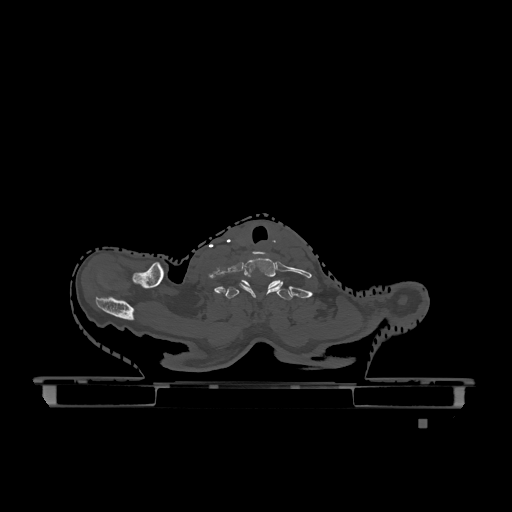
CT including the spine, one axial slice; slice 1017 of 1317 in the series (ordered by position); bone window (W 1800 / L 400 HU); 0.5 mm slice thickness; 512 × 512 image matrix, field of view 500 × 500 mm. Patient: female, 74 years. From the clinical record (not read from this slice): primary cancer: lung; vertebrae with lytic lesions (as recorded): T1, T4, T5, T6, L4, L5.
Structures marked on this image (semi-automatic segmentation, software-assisted and operator-edited):
- T1 vertebra: bounding box [x1, y1, x2, y2] px = [224, 280, 292, 300]